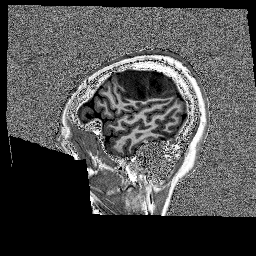
Brain MRI from a brain-tumour surgery series, one sagittal slice. Slice 35 of 176 in the series (ordered by position). 256 × 256 image matrix. Case-level facts recorded for this patient, not image findings: histopathology: Glioblastoma; WHO grade: 4; IDH mutation: no; tumour location: Left Frontal.
Outlined on this slice (expert manual segmentation):
- tumour: bounding box (x1, y1, x2, y2) in pixels: (118, 70, 175, 100)